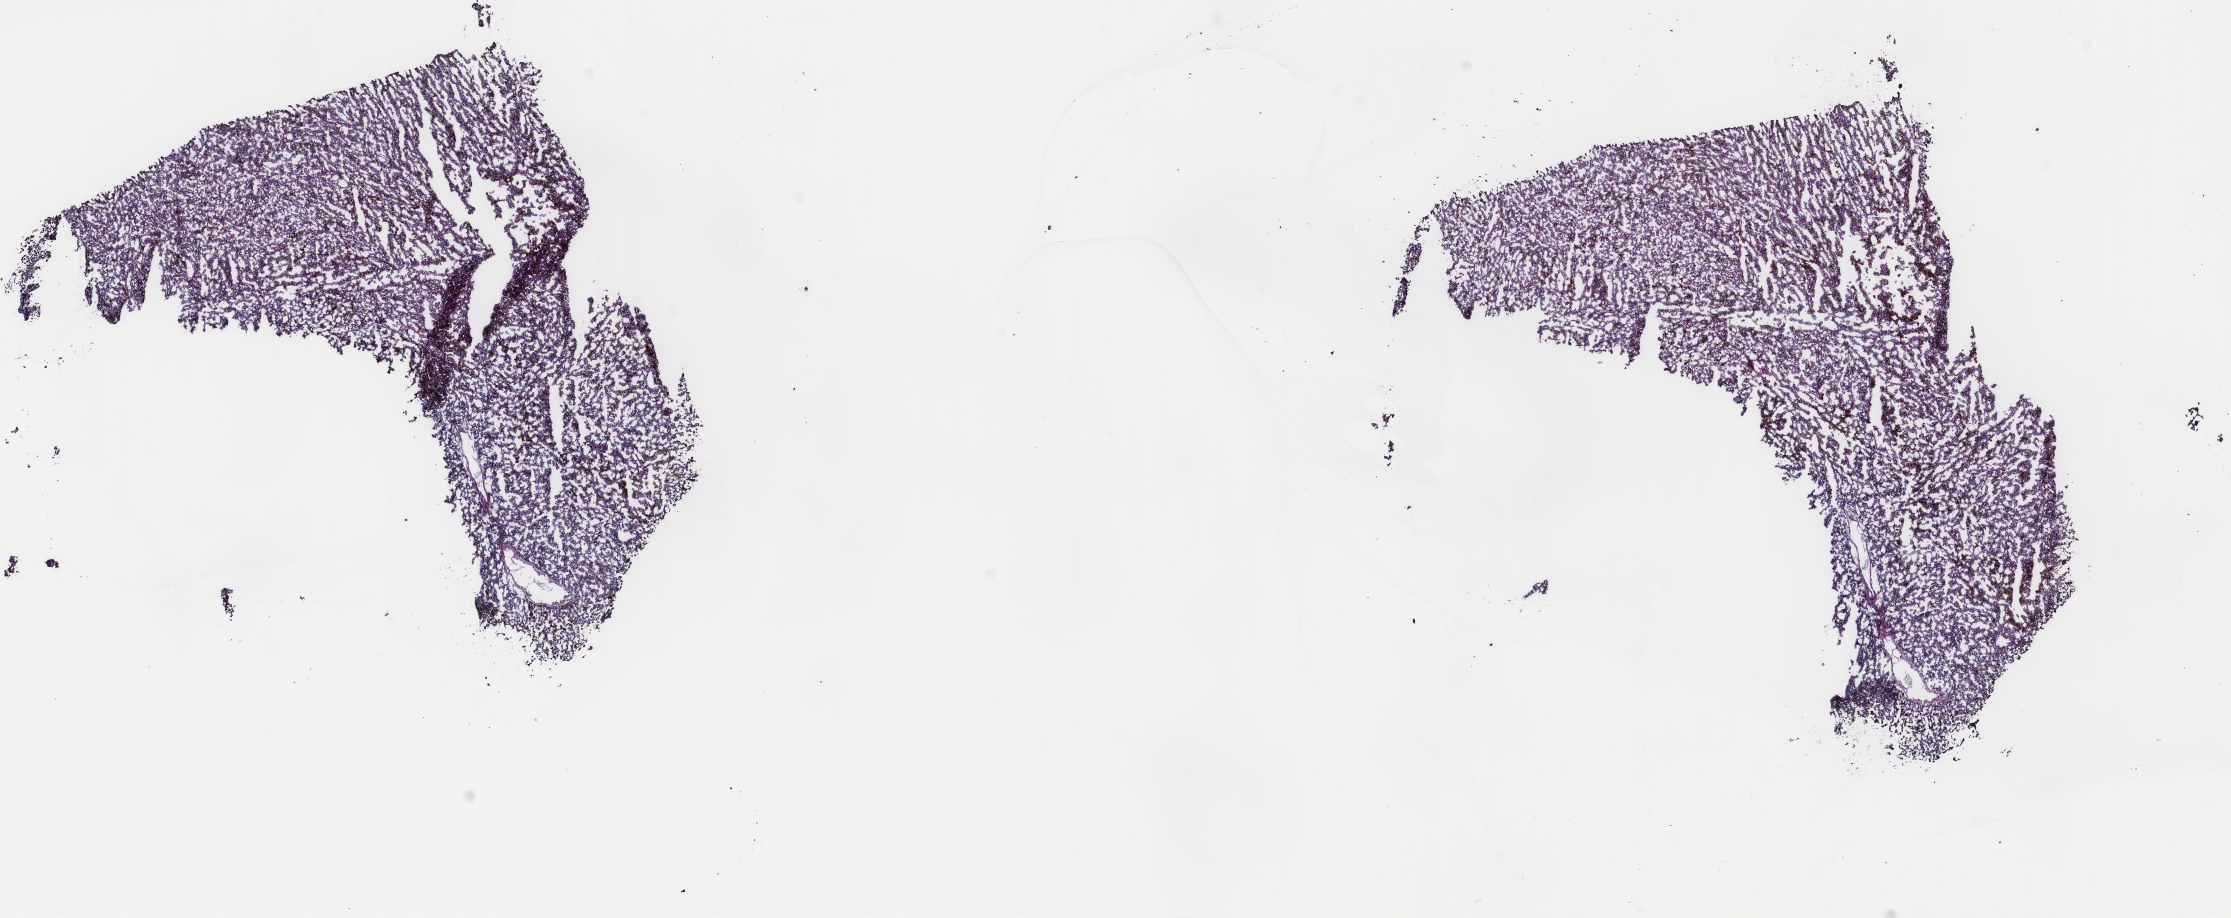
H&E whole-slide image — shown as a low-resolution overview of the whole scanned area (about 17.7 x 7.3 mm). Frozen section from the top of the tissue portion. Metastatic tumour sample, sampled site: lymph nodes of inguinal region or leg. Male patient; age at initial diagnosis 51 years. Slide review estimates, as recorded: tumour cells 100%, tumour nuclei 97%, normal cells 0%, stromal cells 0%, necrosis 0%. Infiltration values recorded for this section: lymphocyte infiltration 0%, monocyte infiltration 0%, neutrophil infiltration 0%.
This section: metastatic tumour tissue. Patient diagnosis: Malignant melanoma, NOS.